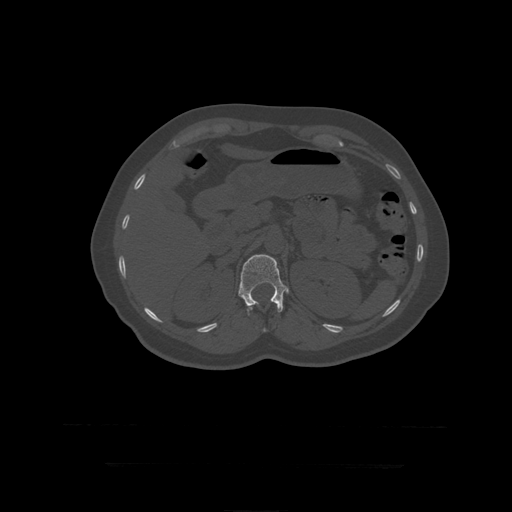
CT including the spine, one axial slice; reconstruction kernel STANDARD; 120 kVp; bone window (W 1800 / L 400 HU); 1.25 mm slice thickness; 512 × 512 image matrix. Patient age 41 years. From the clinical record (not read from this slice): primary cancer: breast.
Structures marked on this image (semi-automatic segmentation, software-assisted and operator-edited):
- L1 vertebra: bounding box <239,255,285,316> (left, top, right, bottom; pixels)
- T12 vertebra: <247,305,267,332>